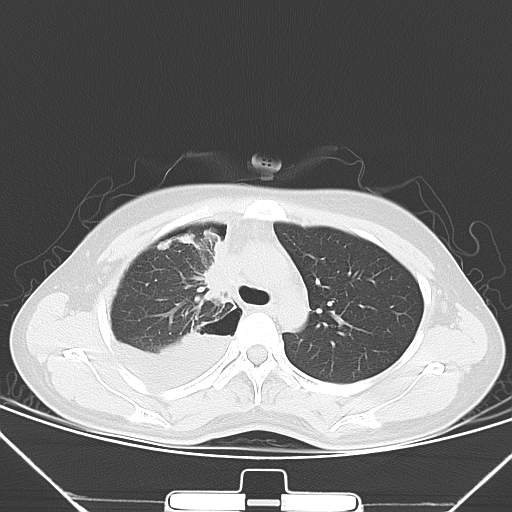
Chest CT, one axial slice. Slice 45 of 62 in the series (ordered by position). Lung window (W 1500 / L -600 HU). 5 mm slice thickness. 512 × 512 image matrix, field of view 343 × 343 mm. Patient: female, 28 years. Case-level facts recorded for this patient, not image findings: clinical TNM (as recorded): T2 N0 M1a.
Annotated regions visible in this slice (rectangle marked by the reading radiologist):
- lung tumour (recorded histology: adenocarcinoma): box from (x=185, y=231) to (x=234, y=301) px